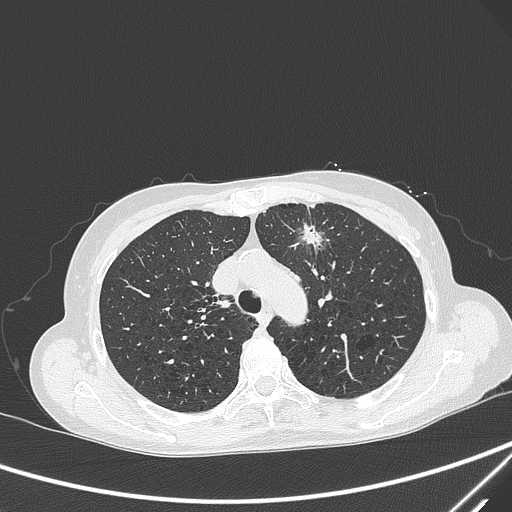
Chest CT, one axial slice; position 224 of 299 along the scan axis; 120 kVp; lung window (W 1500 / L -600 HU); 1 mm slice thickness; 512 × 512 image matrix, field of view 350 × 350 mm. Patient: female, 71 years. From the clinical record (not read from this slice): clinical TNM (as recorded): T1c N0 M0.
Structures marked on this image (bounding box drawn by a radiologist):
- lung tumour (recorded histology: adenocarcinoma): box from (x=292, y=219) to (x=328, y=266) px